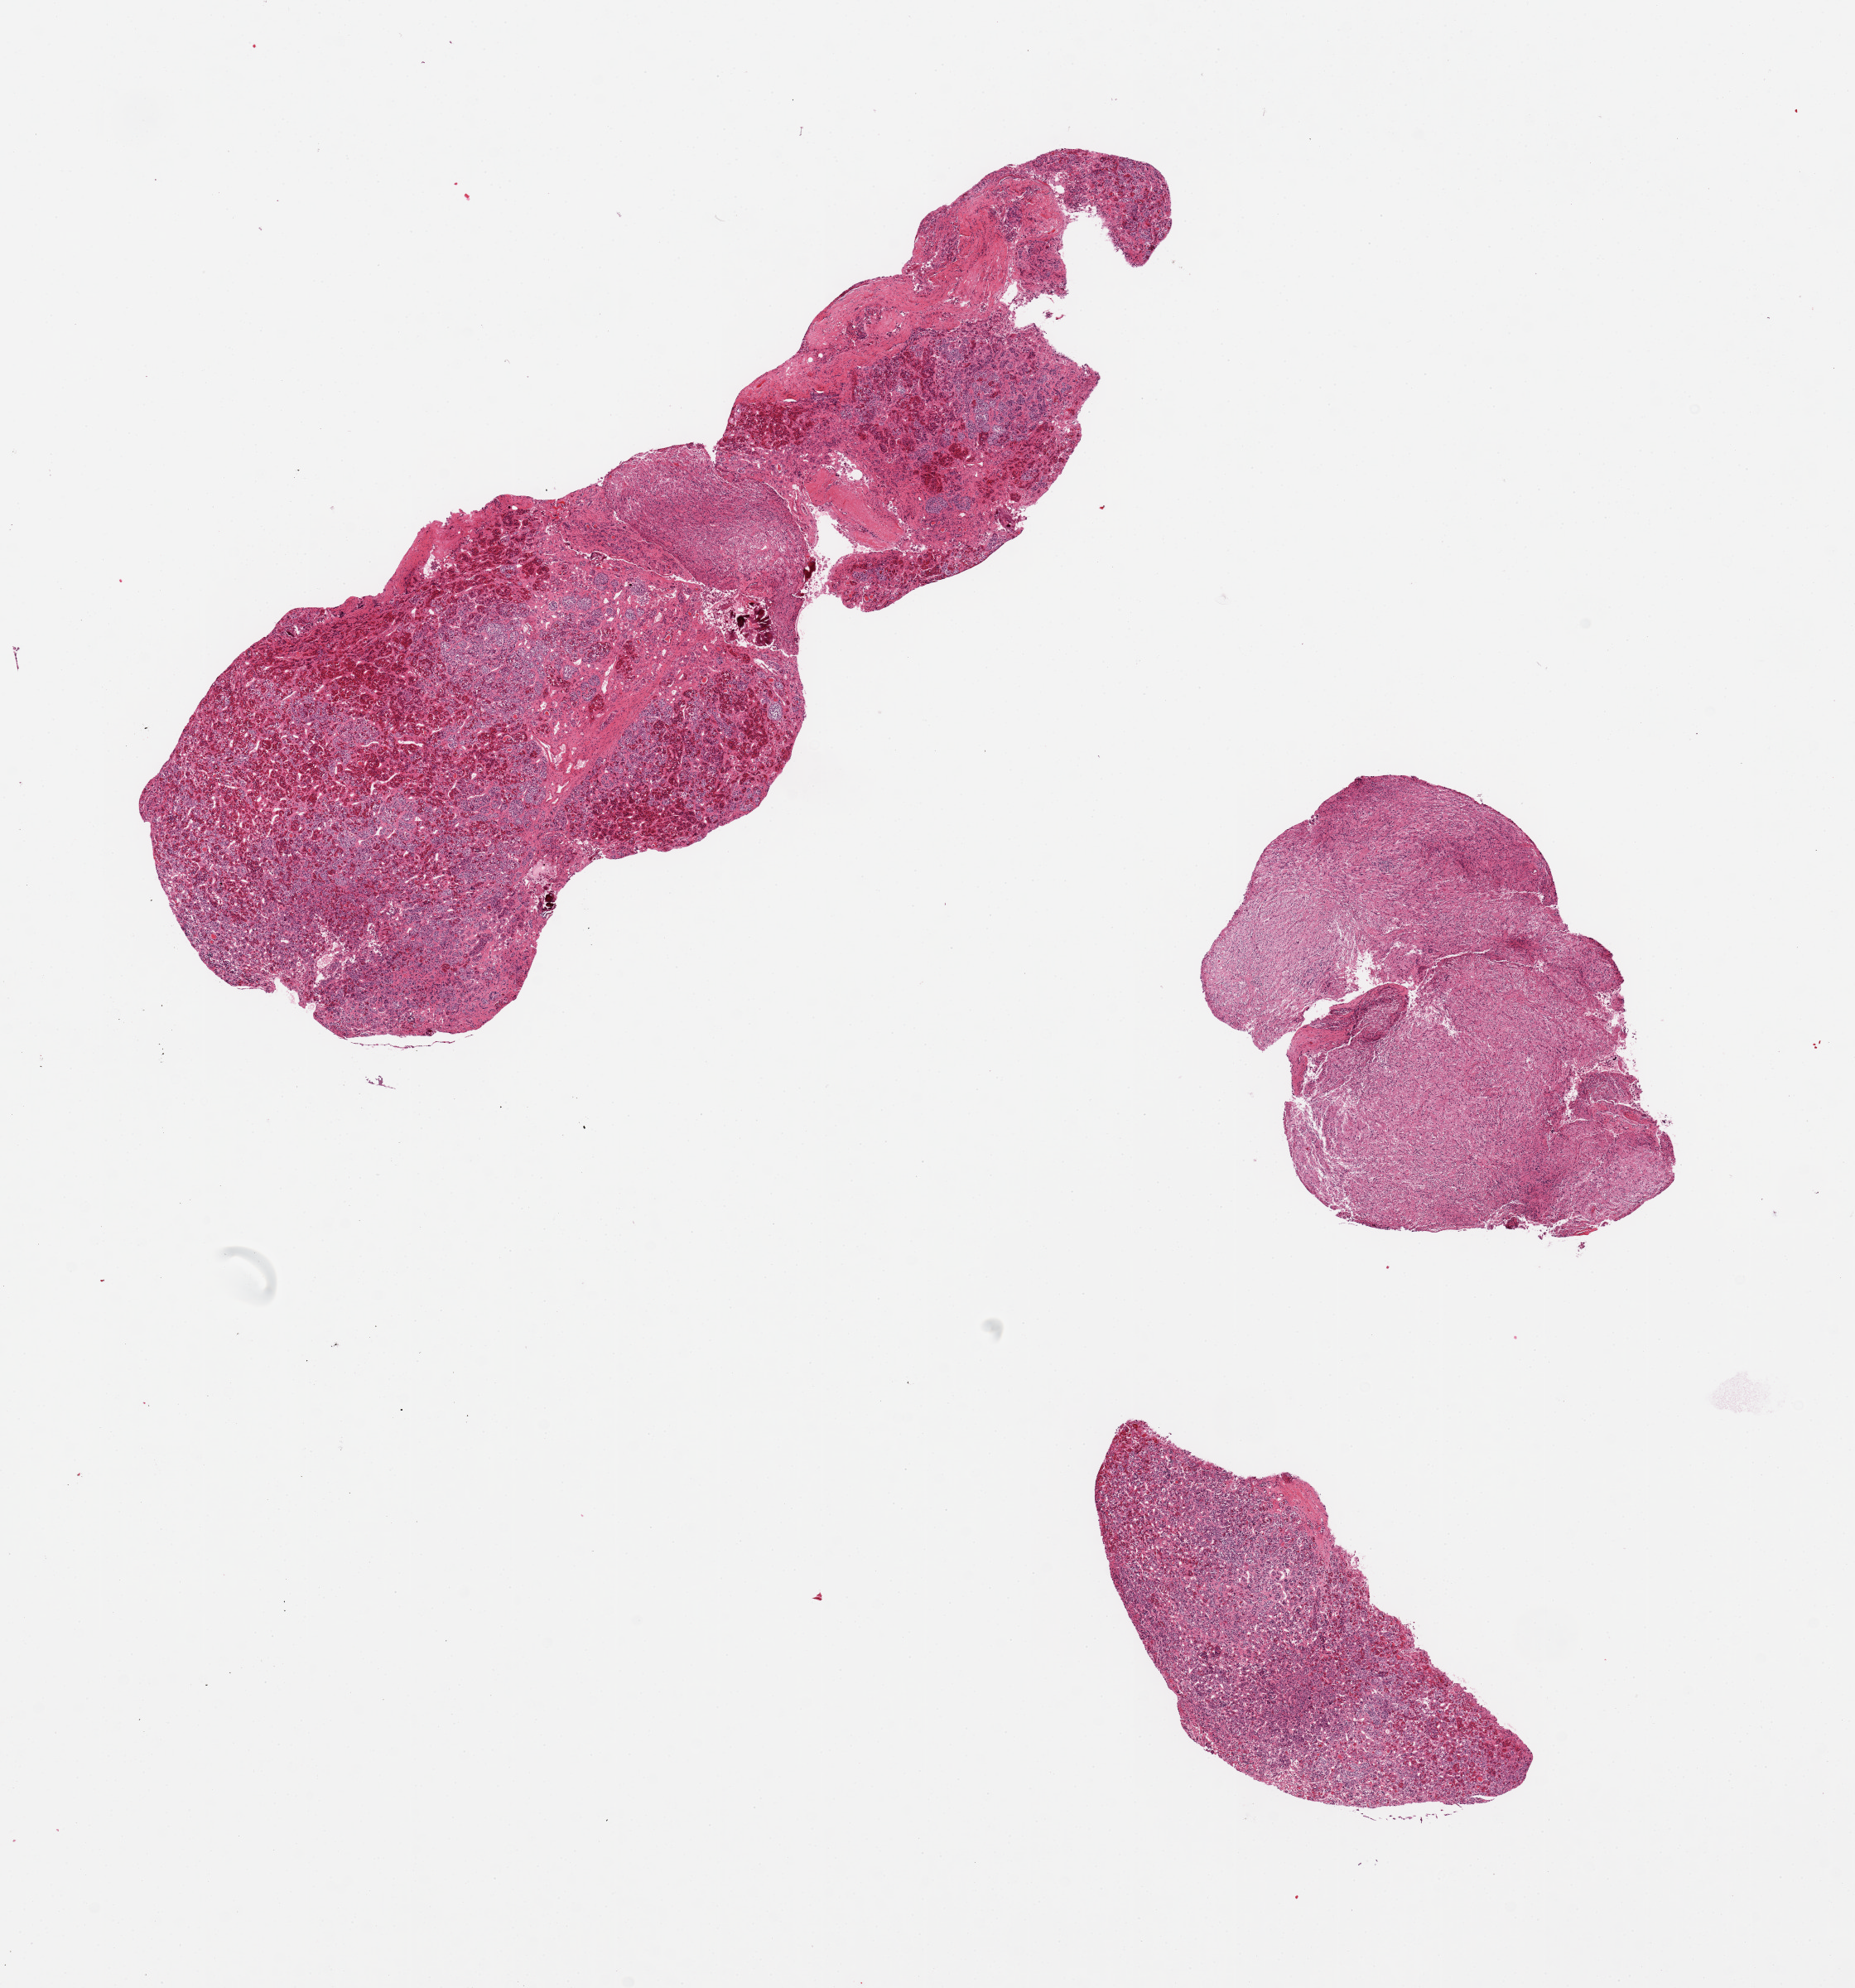
Haematoxylin and eosin whole-slide image — low-resolution overview of the scanned area, about 17.7 x 19.0 mm (from a 20x scan). PAXgene-fixed, paraffin-embedded tissue. Sampled site (target tissue): pituitary. Tissue donor sample.
Review note (as recorded): 3 pieces: largest and 1 smaller piece mostly anterior; other small piece all posterior.